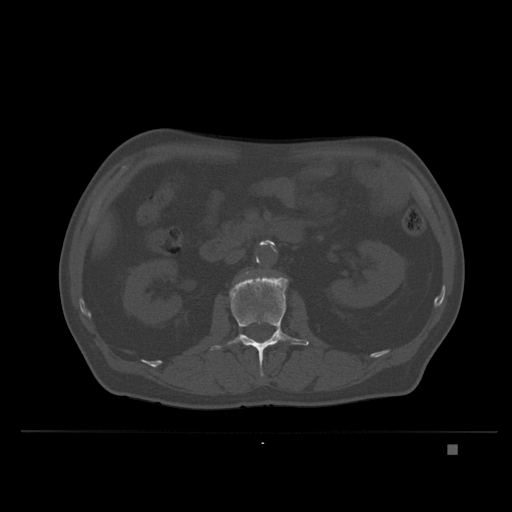
CT including the spine, one axial slice; slice 117 of 435 in the series (ordered by position); bone window (W 1800 / L 400 HU); 1.5 mm slice thickness; 512 × 512 image matrix, field of view 434 × 434 mm. Patient: male, 73 years. From the clinical record (not read from this slice): primary cancer: skin.
Structures marked on this image (semi-automatically segmented with operator editing):
- L2 vertebra: bounding box [x1, y1, x2, y2] px = [210, 276, 309, 376]